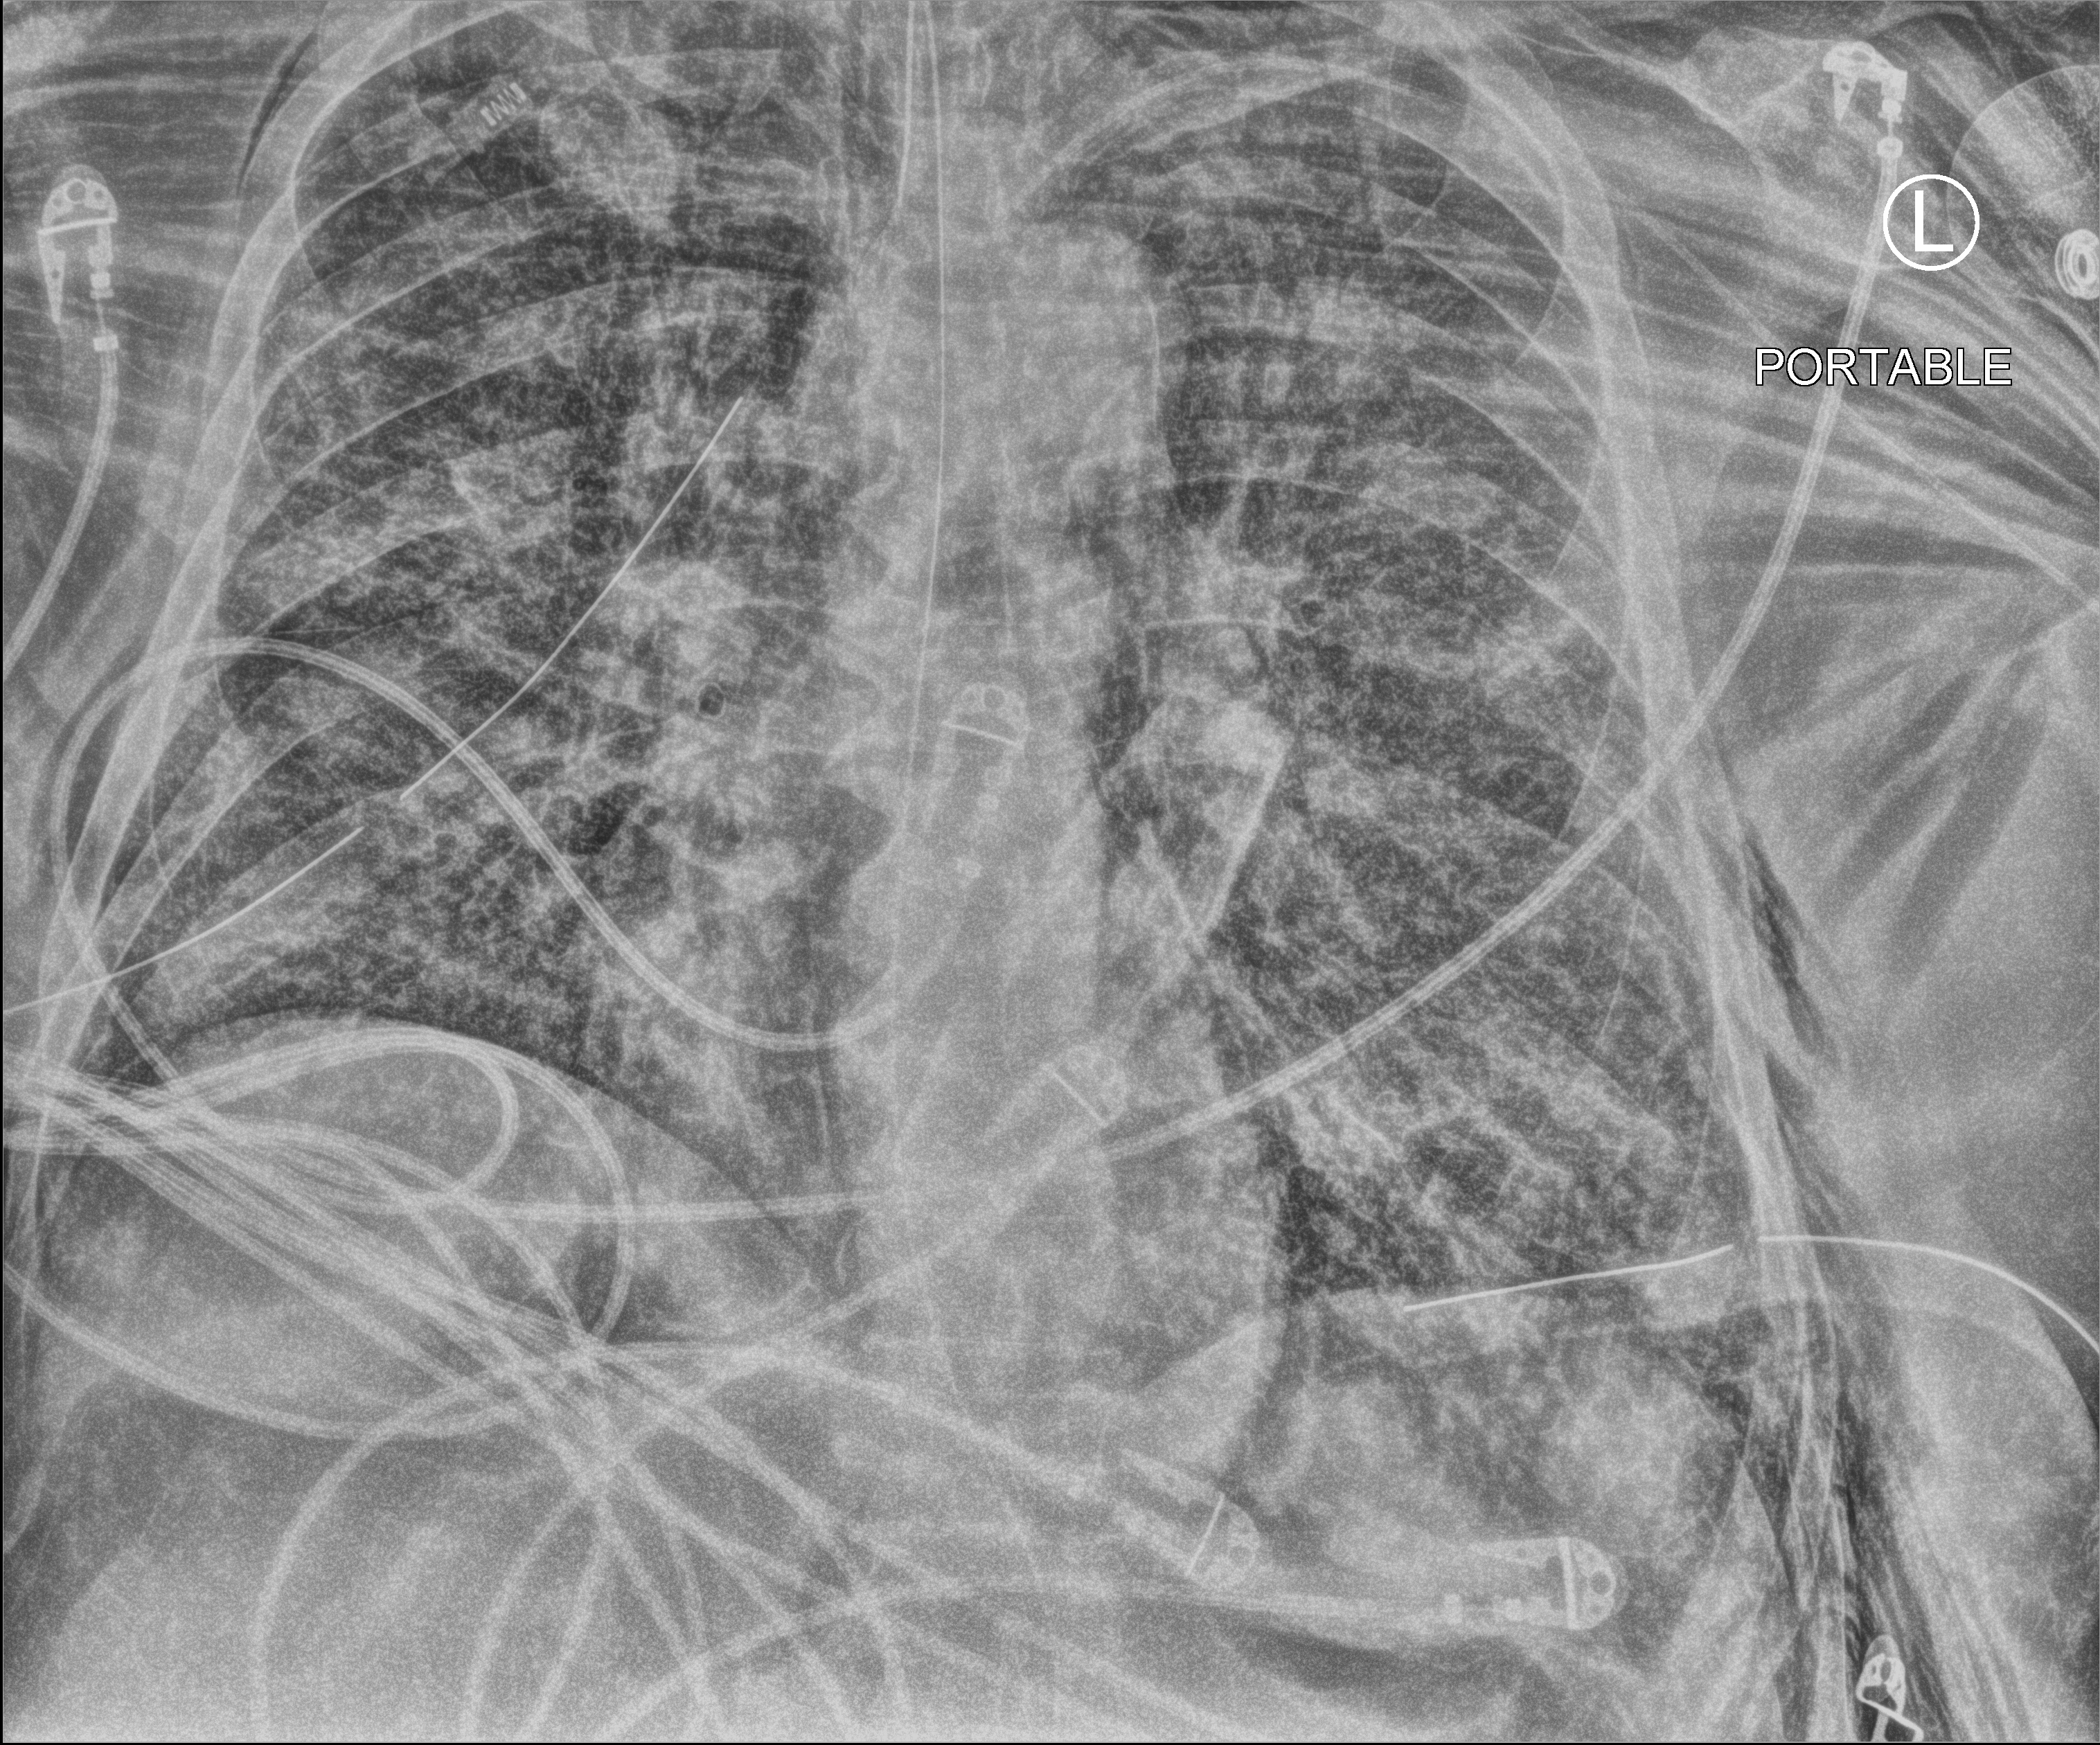
Chest X-ray (portable), anteroposterior (AP) projection. Adult patient hospitalised with COVID-19, age 18–59 years.
From the hospital-stay record, not from the radiograph (when in the stay this image was taken is not recorded): length of hospital stay: 28 days; admitted to intensive care during this hospital stay: yes.